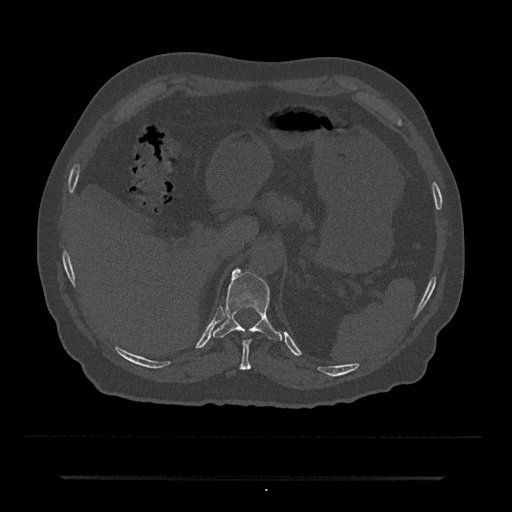
CT including the spine, one axial slice; position 190 of 797 along the scan axis; 120 kVp; bone window (W 1800 / L 400 HU); 0.5 mm slice thickness; 512 × 512 image matrix. Male patient, age 69 years. From the clinical record (not read from this slice): primary cancer: prostate.
Outlined on this slice (semi-automatic segmentation, software-assisted and operator-edited):
- T10 vertebra: bounding box (x1, y1, x2, y2) in pixels: (240, 339, 252, 369)
- T11 vertebra: (213, 268, 283, 341)